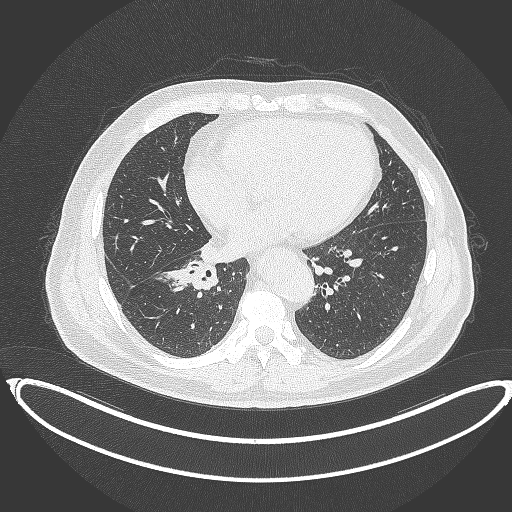
Chest CT, one axial slice. Position 165 of 387 along the scan axis. 120 kVp. Lung window (W 1500 / L -600 HU). 1 mm slice thickness. 512 × 512 image matrix. Male patient, age 61 years. Case-level facts recorded for this patient, not image findings: clinical TNM (as recorded): T1b N1 M0.
Outlined on this slice (rectangle marked by the reading radiologist):
- lung tumour (recorded histology: squamous cell carcinoma): bounding box <161,255,221,295> (left, top, right, bottom; pixels)